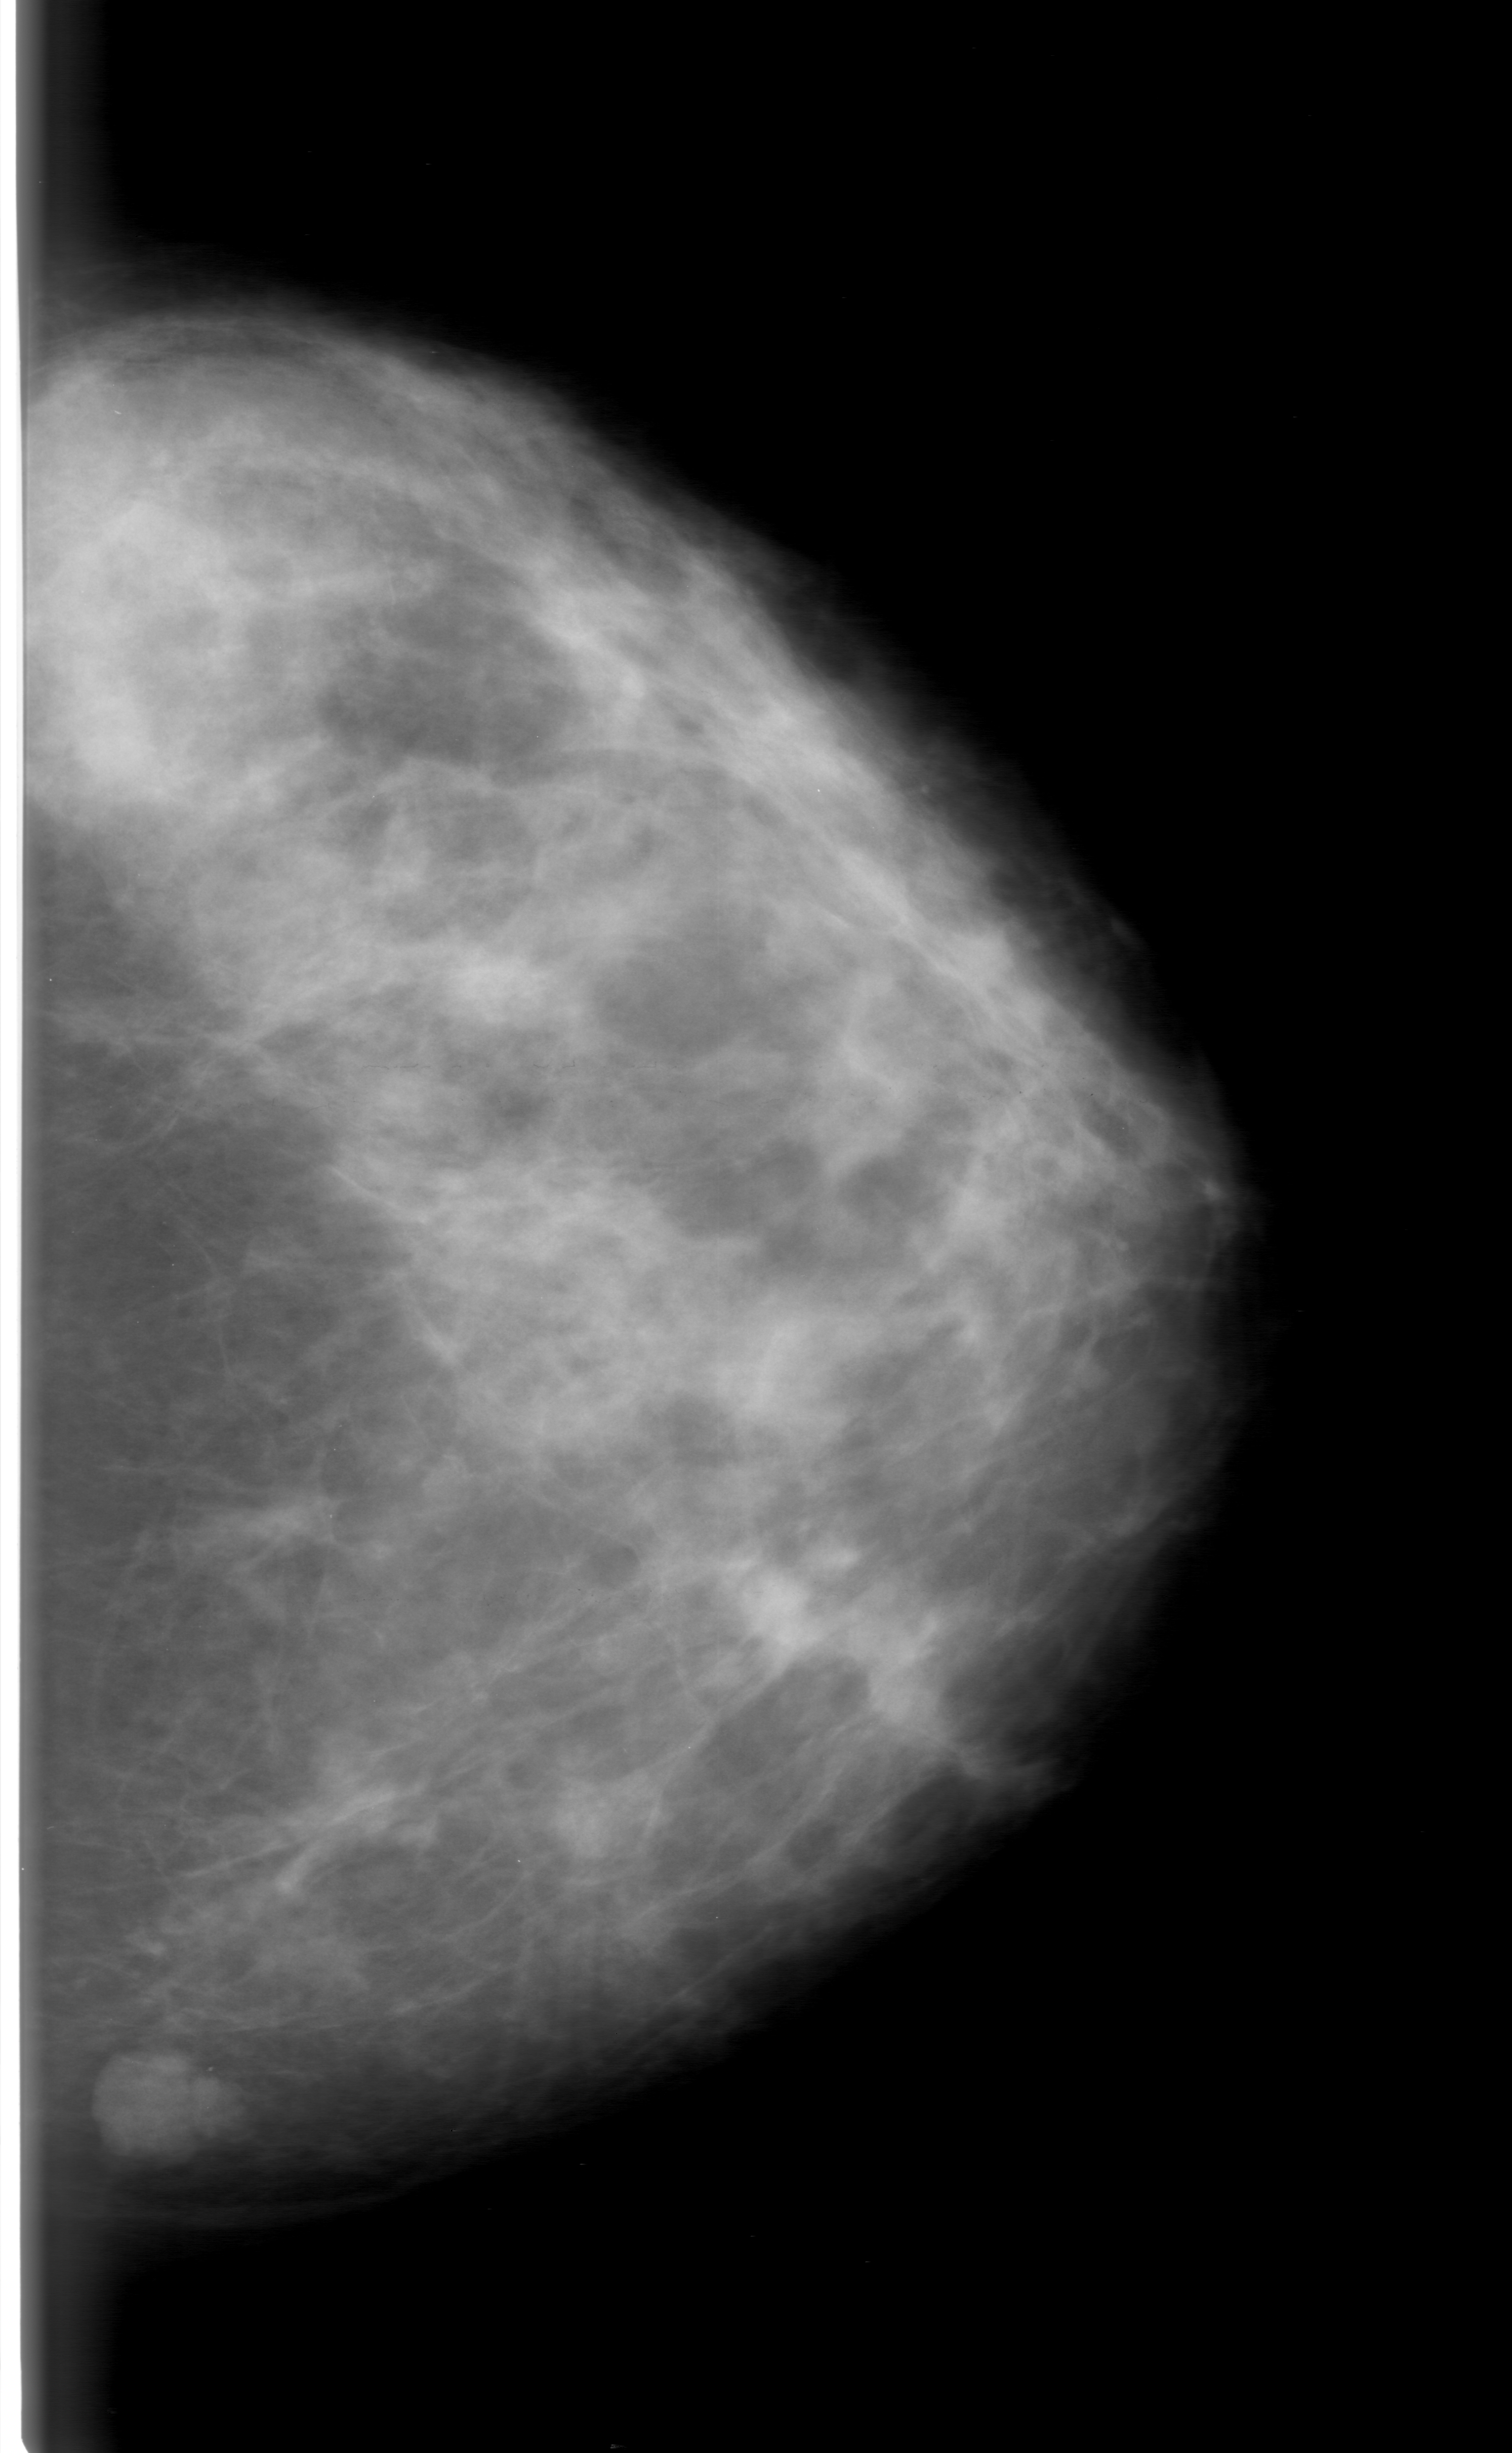
Mammogram (digitized film), left breast, CC view, breast composition: heterogeneously dense (BI-RADS density category 3 of 4).
Mass, shape lobulated, margins microlobulated; BI-RADS assessment category 3; pathology (as recorded): benign.